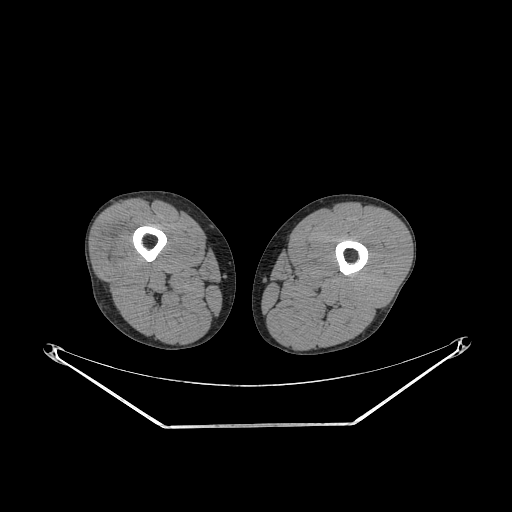
CT of an extremity soft-tissue mass (from a PET/CT study), one axial slice. Position 217 of 267 along the scan axis. Reconstruction kernel STANDARD. Soft-tissue window (W 400 / L 40 HU). 3.75 mm slice thickness. 512 × 512 image matrix, field of view 500 × 500 mm. Male patient. From the clinical record (not read from this slice): histological type: poorly differentiated synovial sarcoma; grade: high; site of the primary tumour: right buttock.
Annotated regions visible in this slice (expert contour drawn on MRI and transferred to this co-registered scan by the dataset authors):
- gross tumour volume including surrounding oedema: box from (x=107, y=238) to (x=131, y=266) px